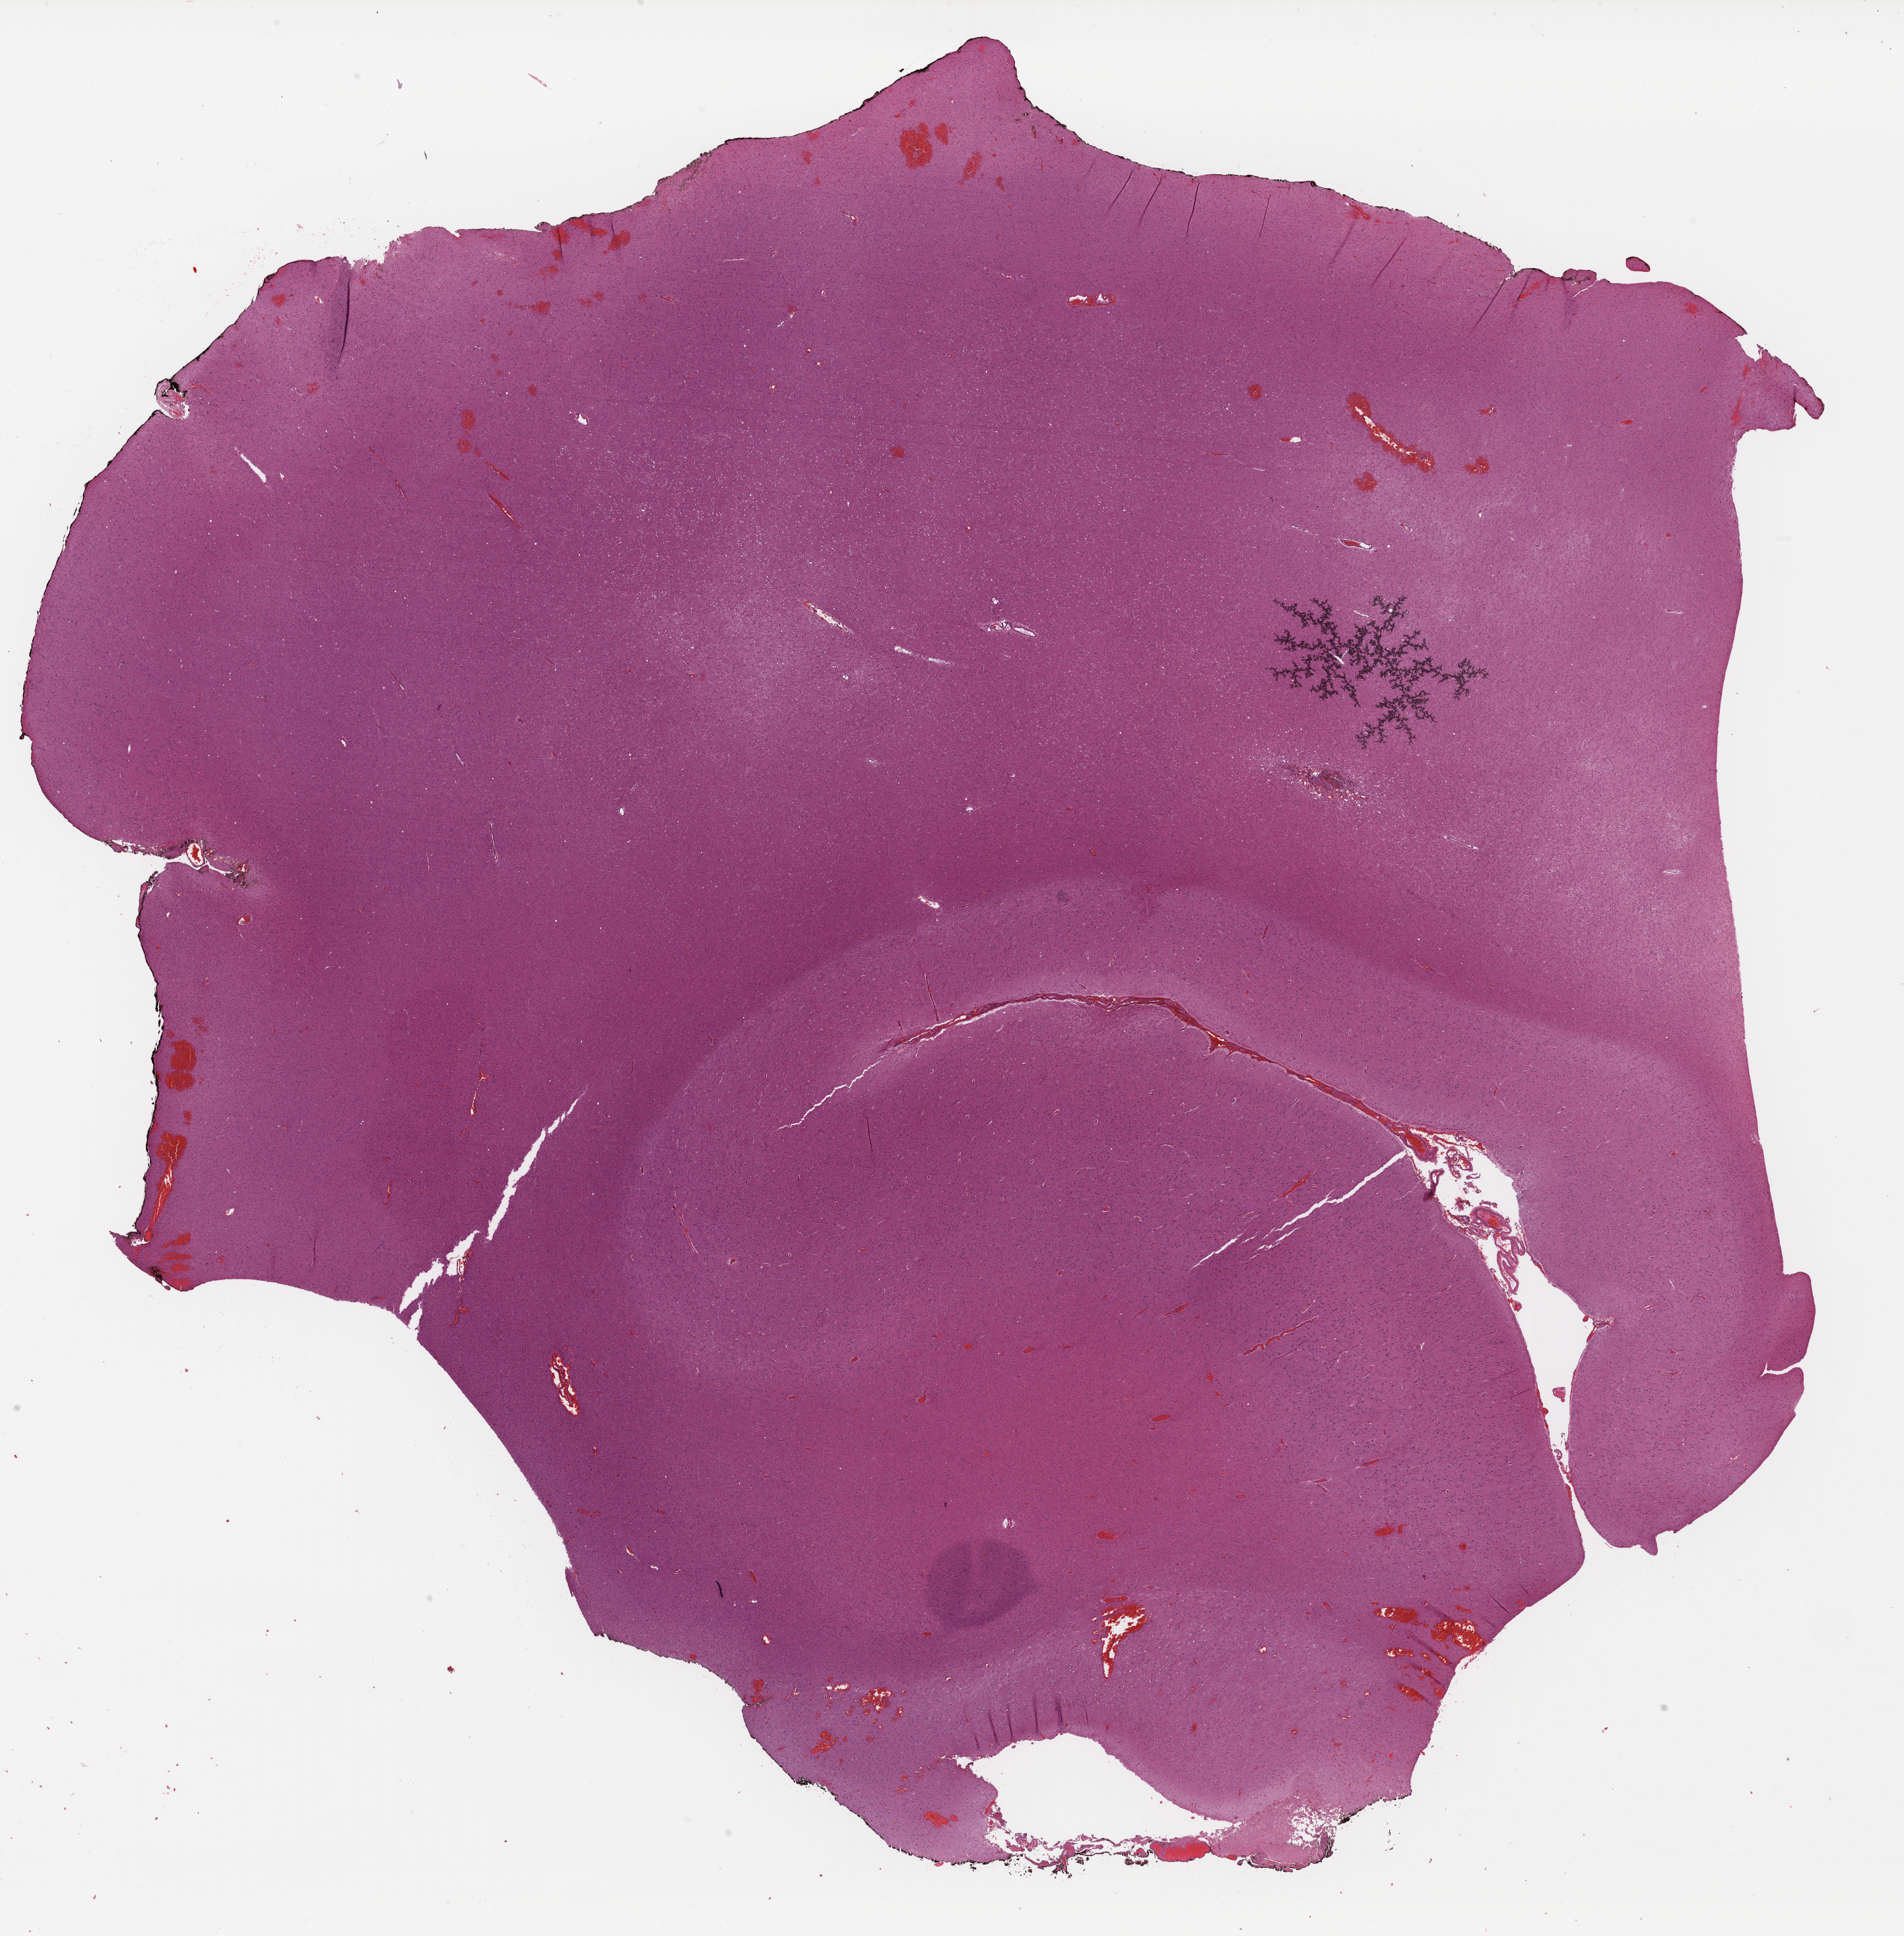
H&E whole-slide image, low-resolution overview of the scanned area, about 22.7 x 23.1 mm (from a 40x scan), FFPE section, primary tumour sample from the brain. Female patient; age at initial diagnosis 61 years. Histologic grade: G2 (moderately differentiated).
Laterality: left. Pathologic diagnosis: Astrocytoma, NOS (cerebrum).